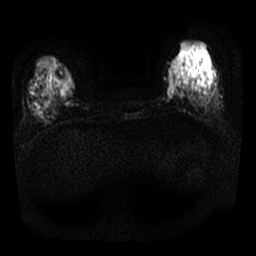
Breast MRI, one axial slice. Diffusion-weighted series; image 2 of 4 stored at this slice position (different b-values; order by instance number). 1.5 T. 4 mm slice thickness. 256 × 256 image matrix, field of view 300 × 300 mm. Female patient.
Annotated regions visible in this slice (expert manual segmentation):
- tumour on diffusion-weighted imaging: box from (x=170, y=79) to (x=174, y=99) px